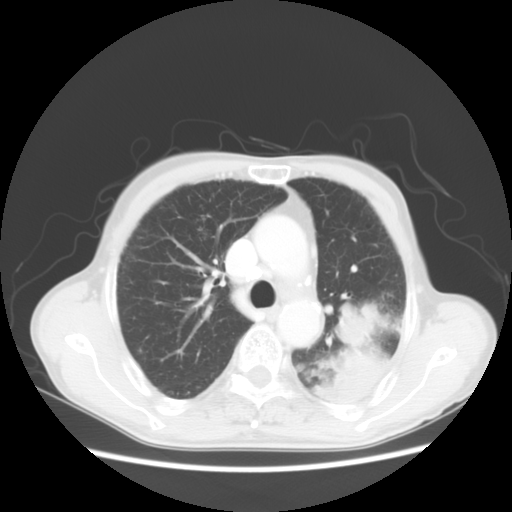
Chest CT, one axial slice. Position 36 of 51 along the scan axis. Reconstruction kernel STANDARD. Lung window (W 1500 / L -600 HU). 5 mm slice thickness. 512 × 512 image matrix. Male patient, age 64 years. Case-level facts recorded for this patient, not image findings: clinical TNM (as recorded): T4 N0 M0.
Annotated regions visible in this slice (bounding box drawn by a radiologist):
- lung tumour (recorded histology: squamous cell carcinoma): bounding box [x1, y1, x2, y2] px = [319, 300, 392, 399]